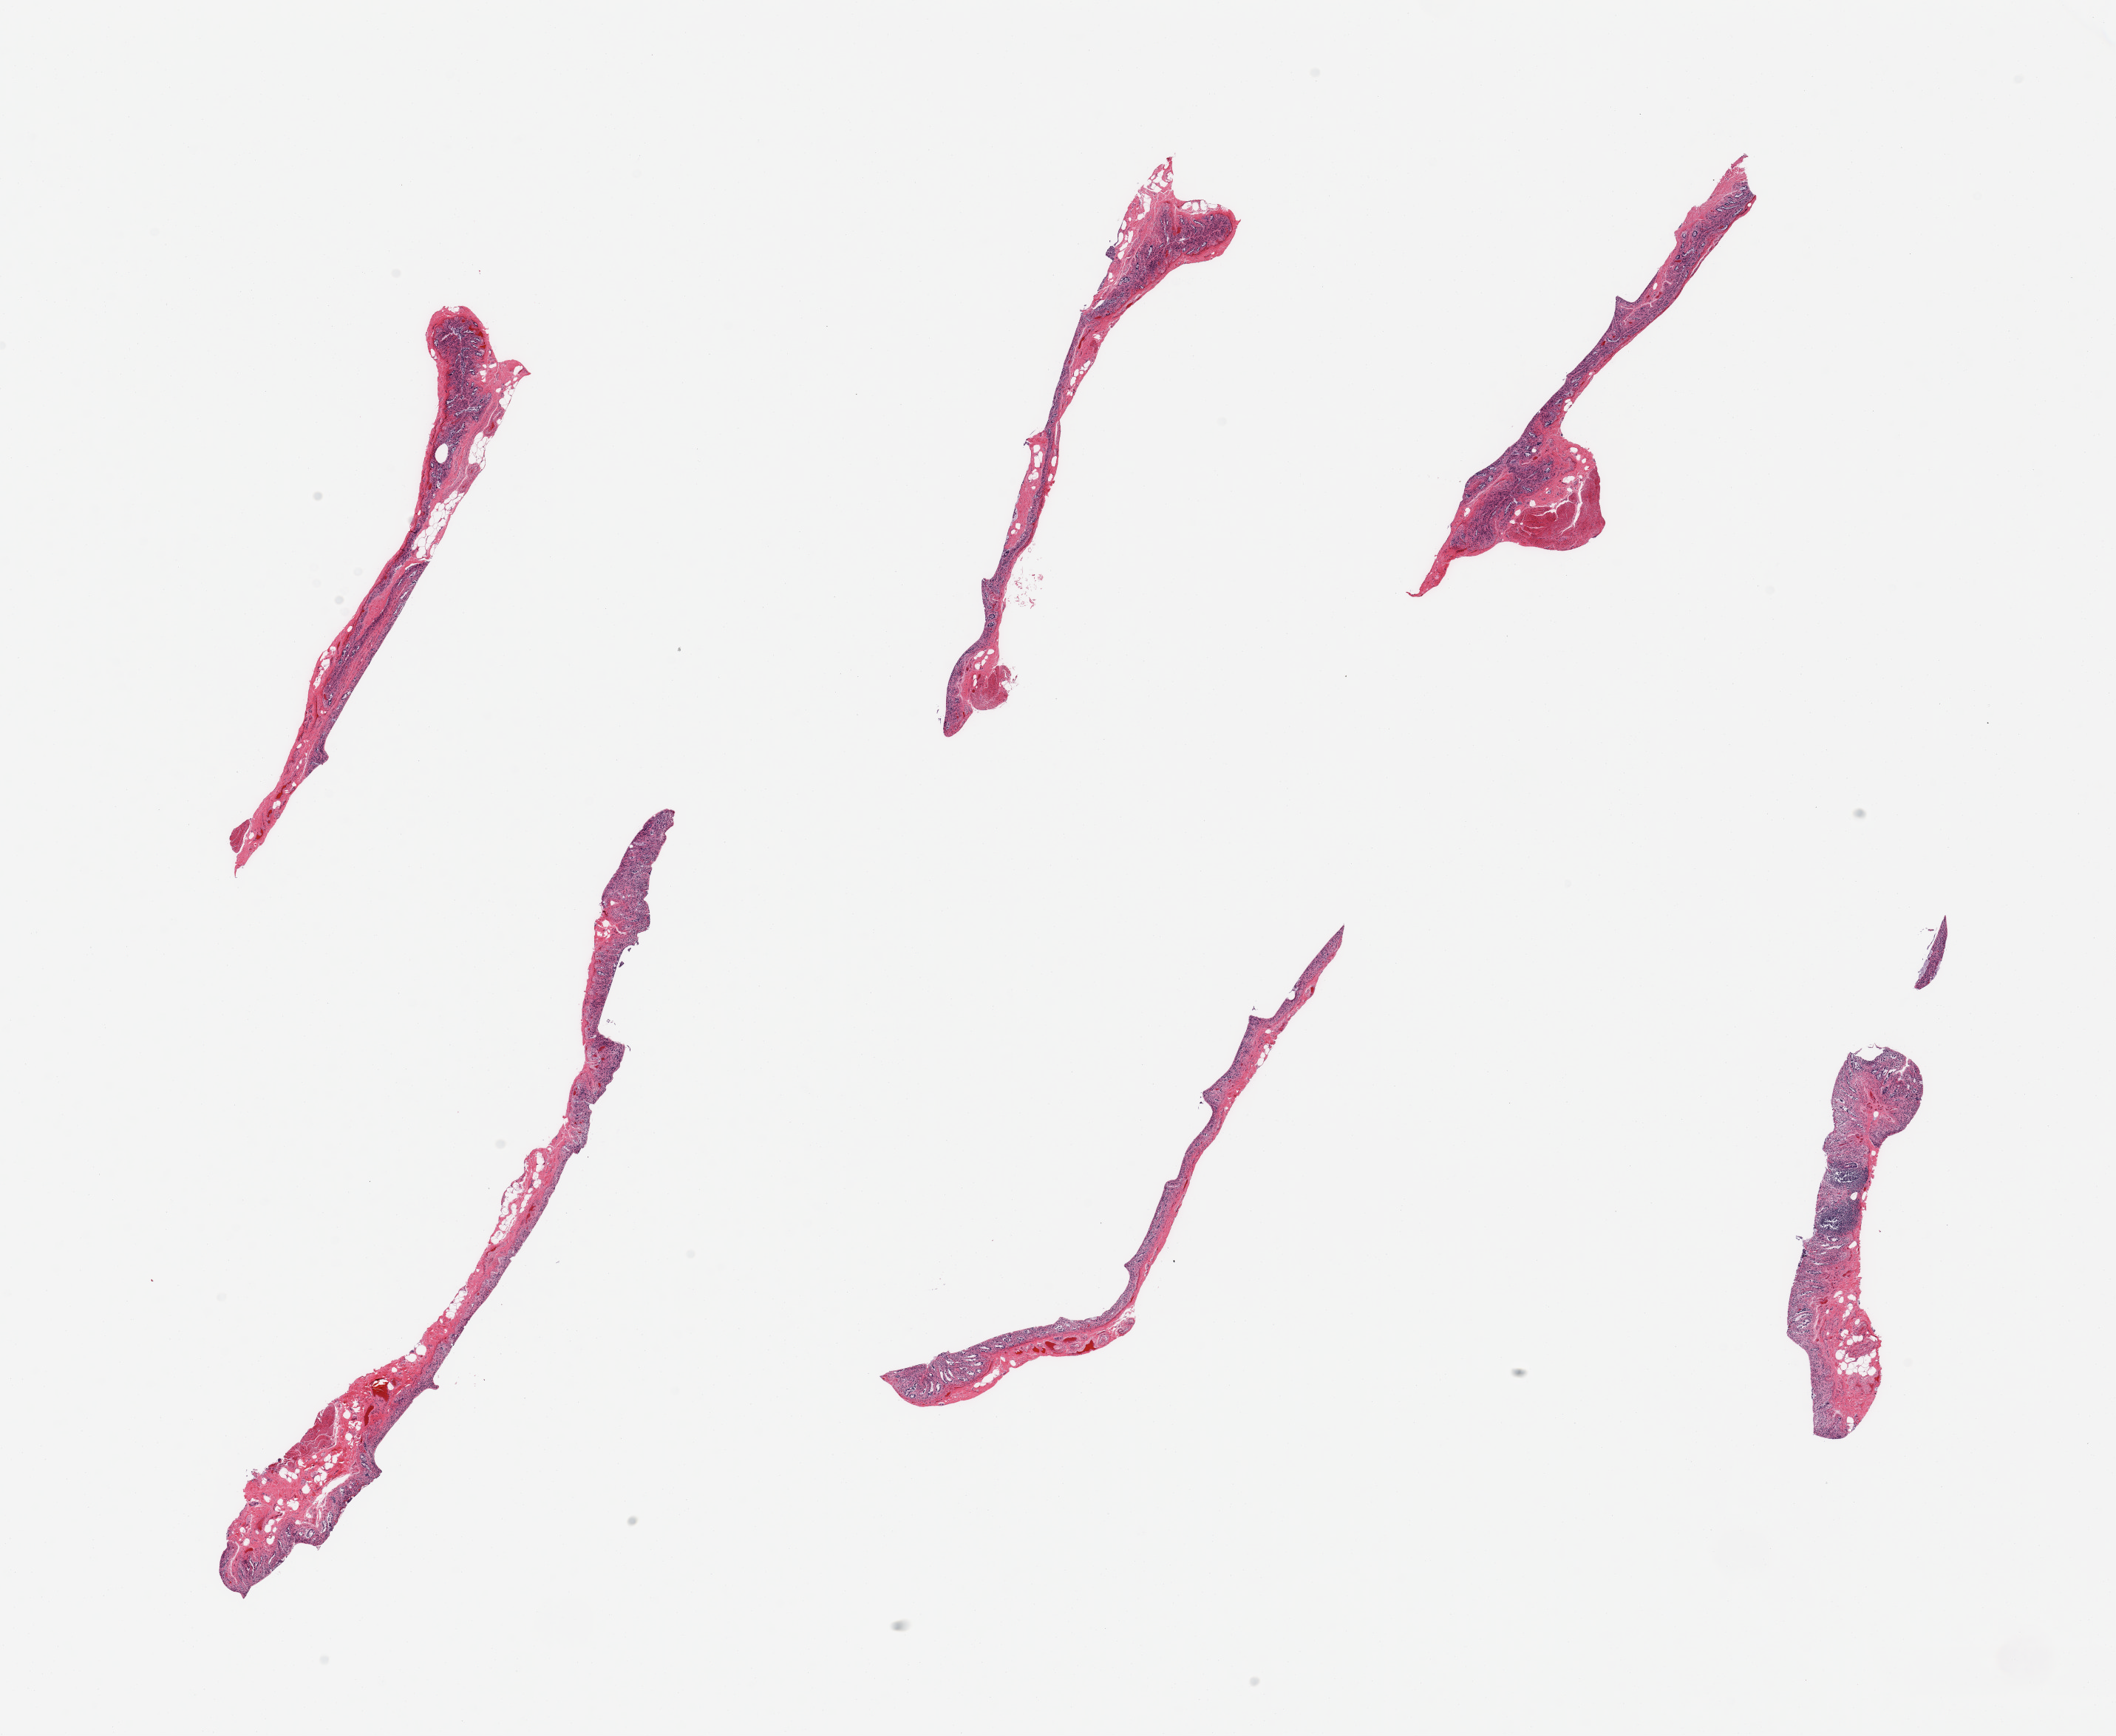
Haematoxylin and eosin whole-slide image — a low-resolution overview of the entire scanned area, about 22.6 x 18.6 mm (acquisition: 20x scan); PAXgene-fixed paraffin-embedded (PFPE) section; section of transverse colon (target tissue); donor tissue sample. Donor: male.
- reviewer comment on this tissue sample: 6 pieces; mostly autolyzed mucosa, some muscularis